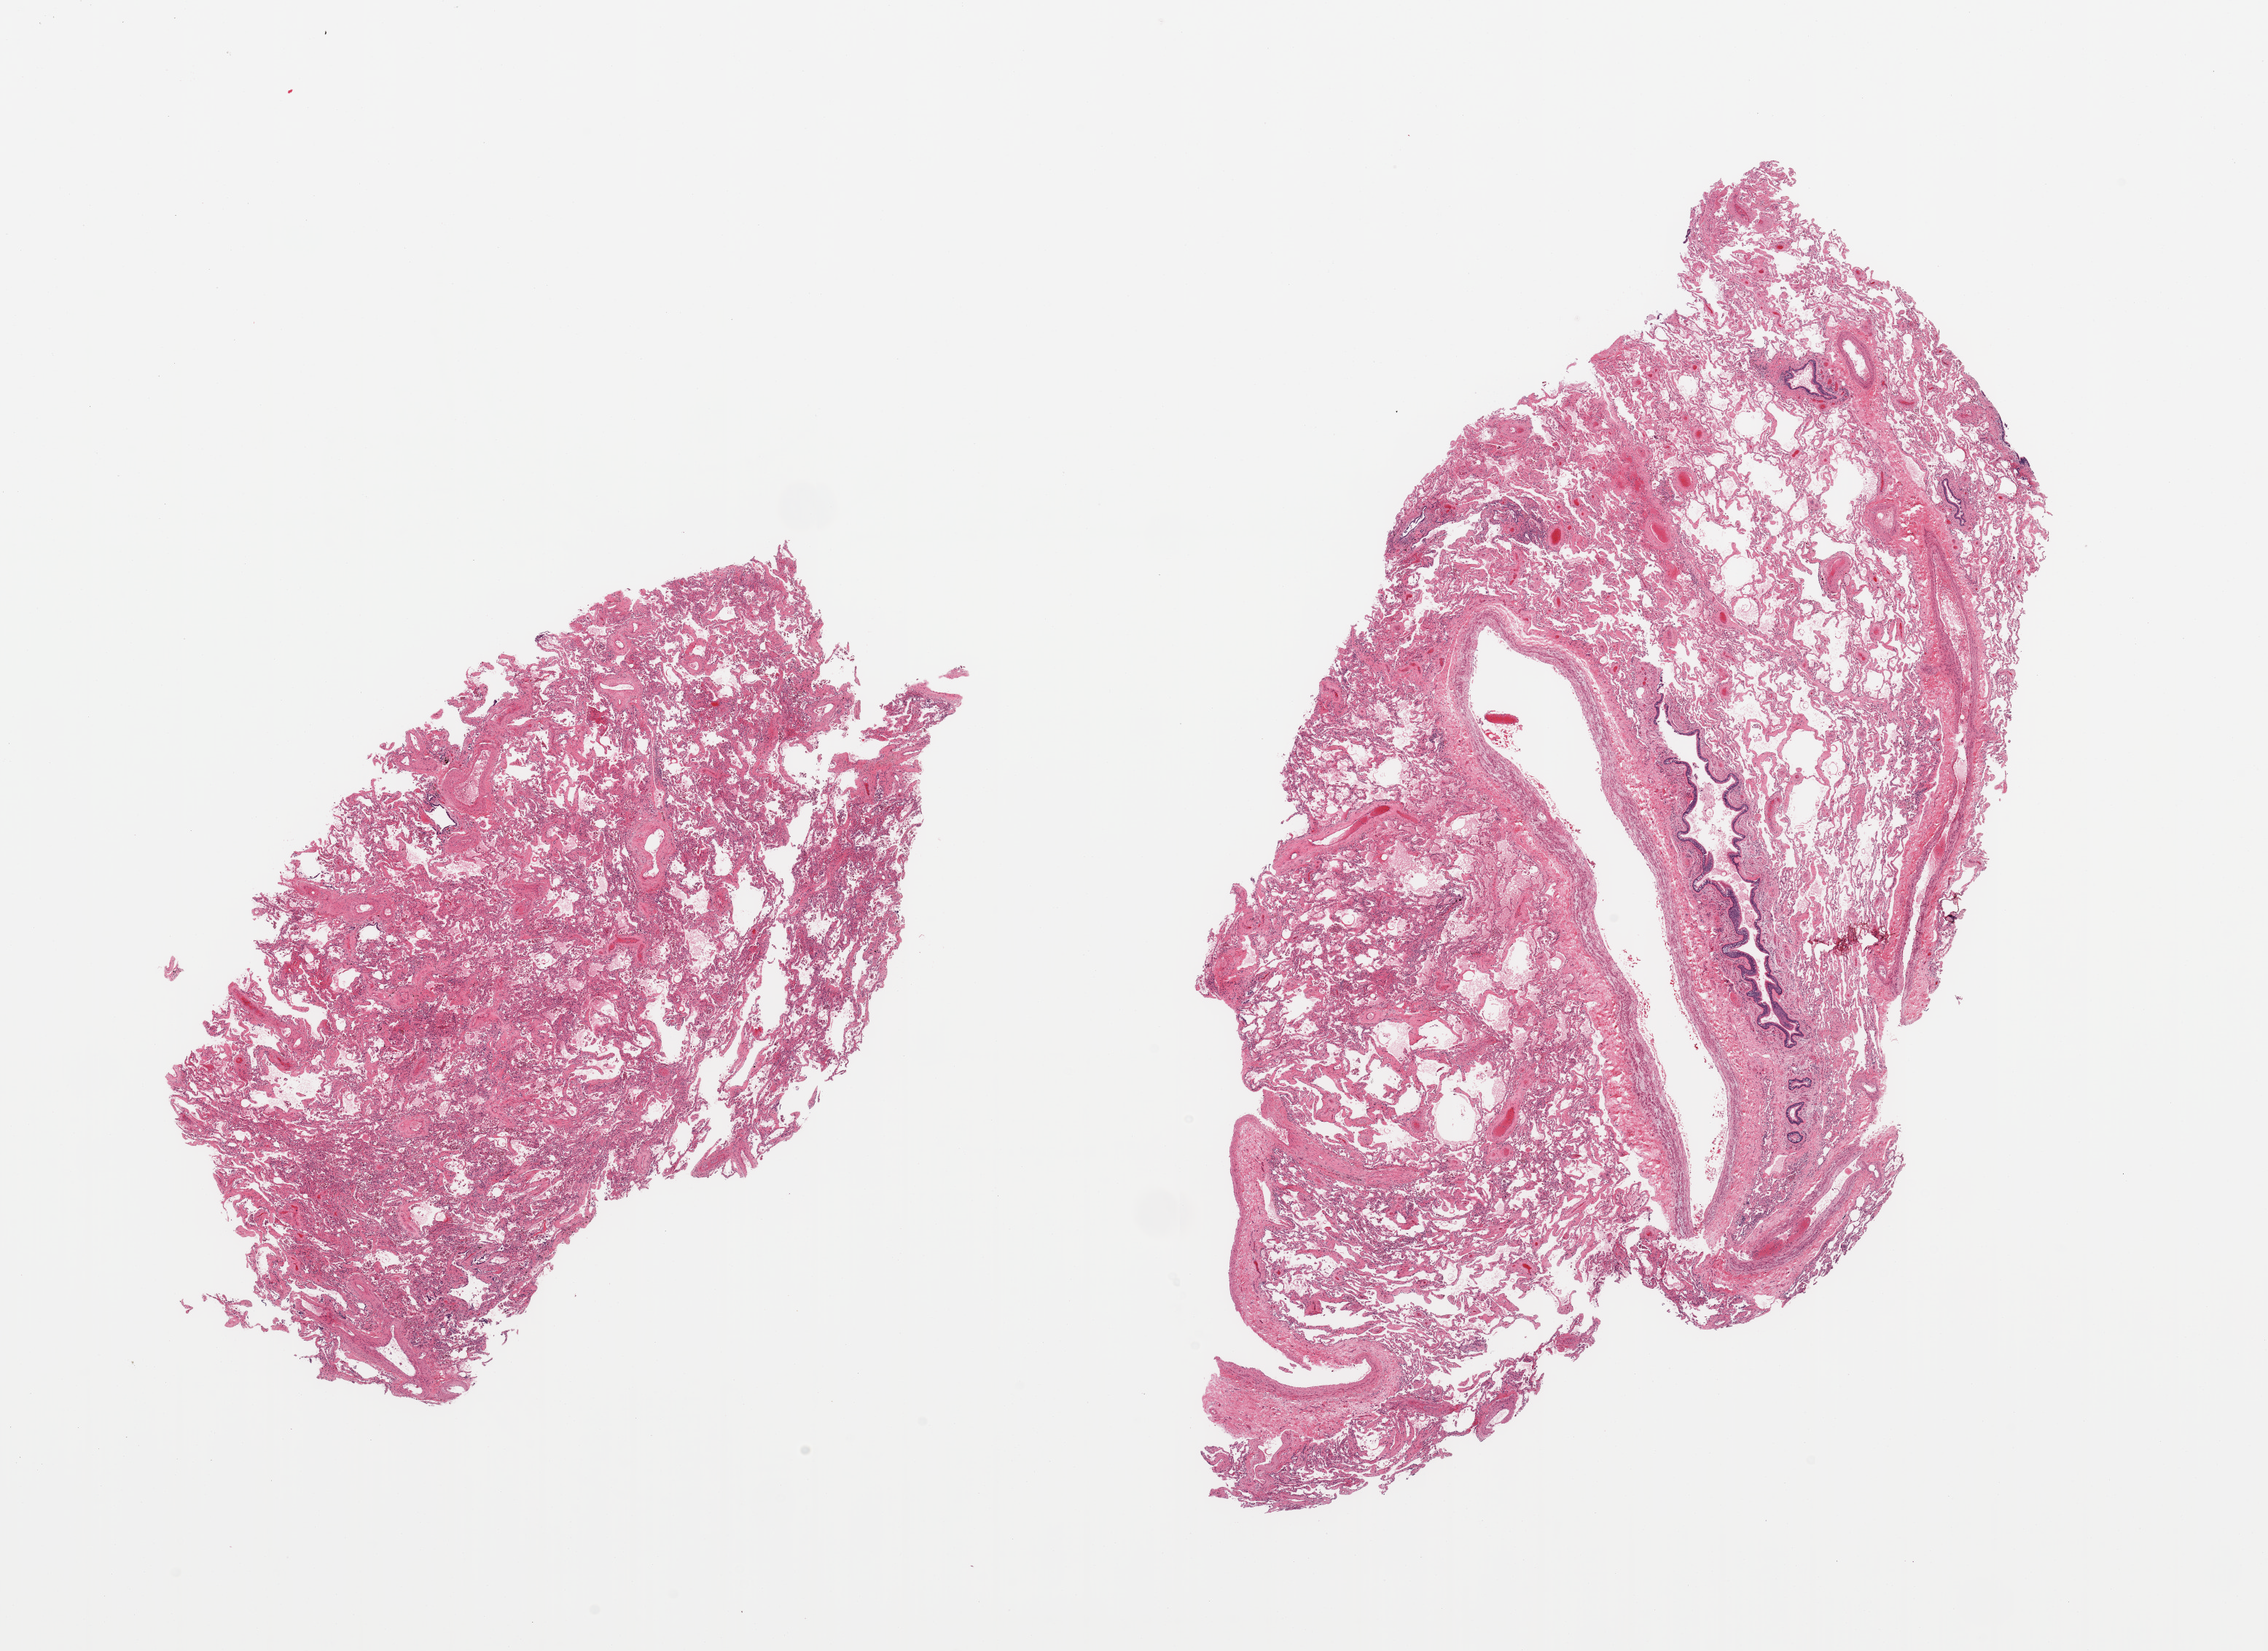
Whole-slide image, haematoxylin and eosin stain, brightfield — low-resolution overview of the scanned area, about 24.6 x 17.9 mm. PAXgene-fixed, paraffin-embedded tissue. Sampled site (target tissue): lung. Donor tissue sample. Donor: female.
- review note (as recorded): 2 pieces; moderate emphysema and fibrosis with thick walled vessels & pigmented alveolar macrophages